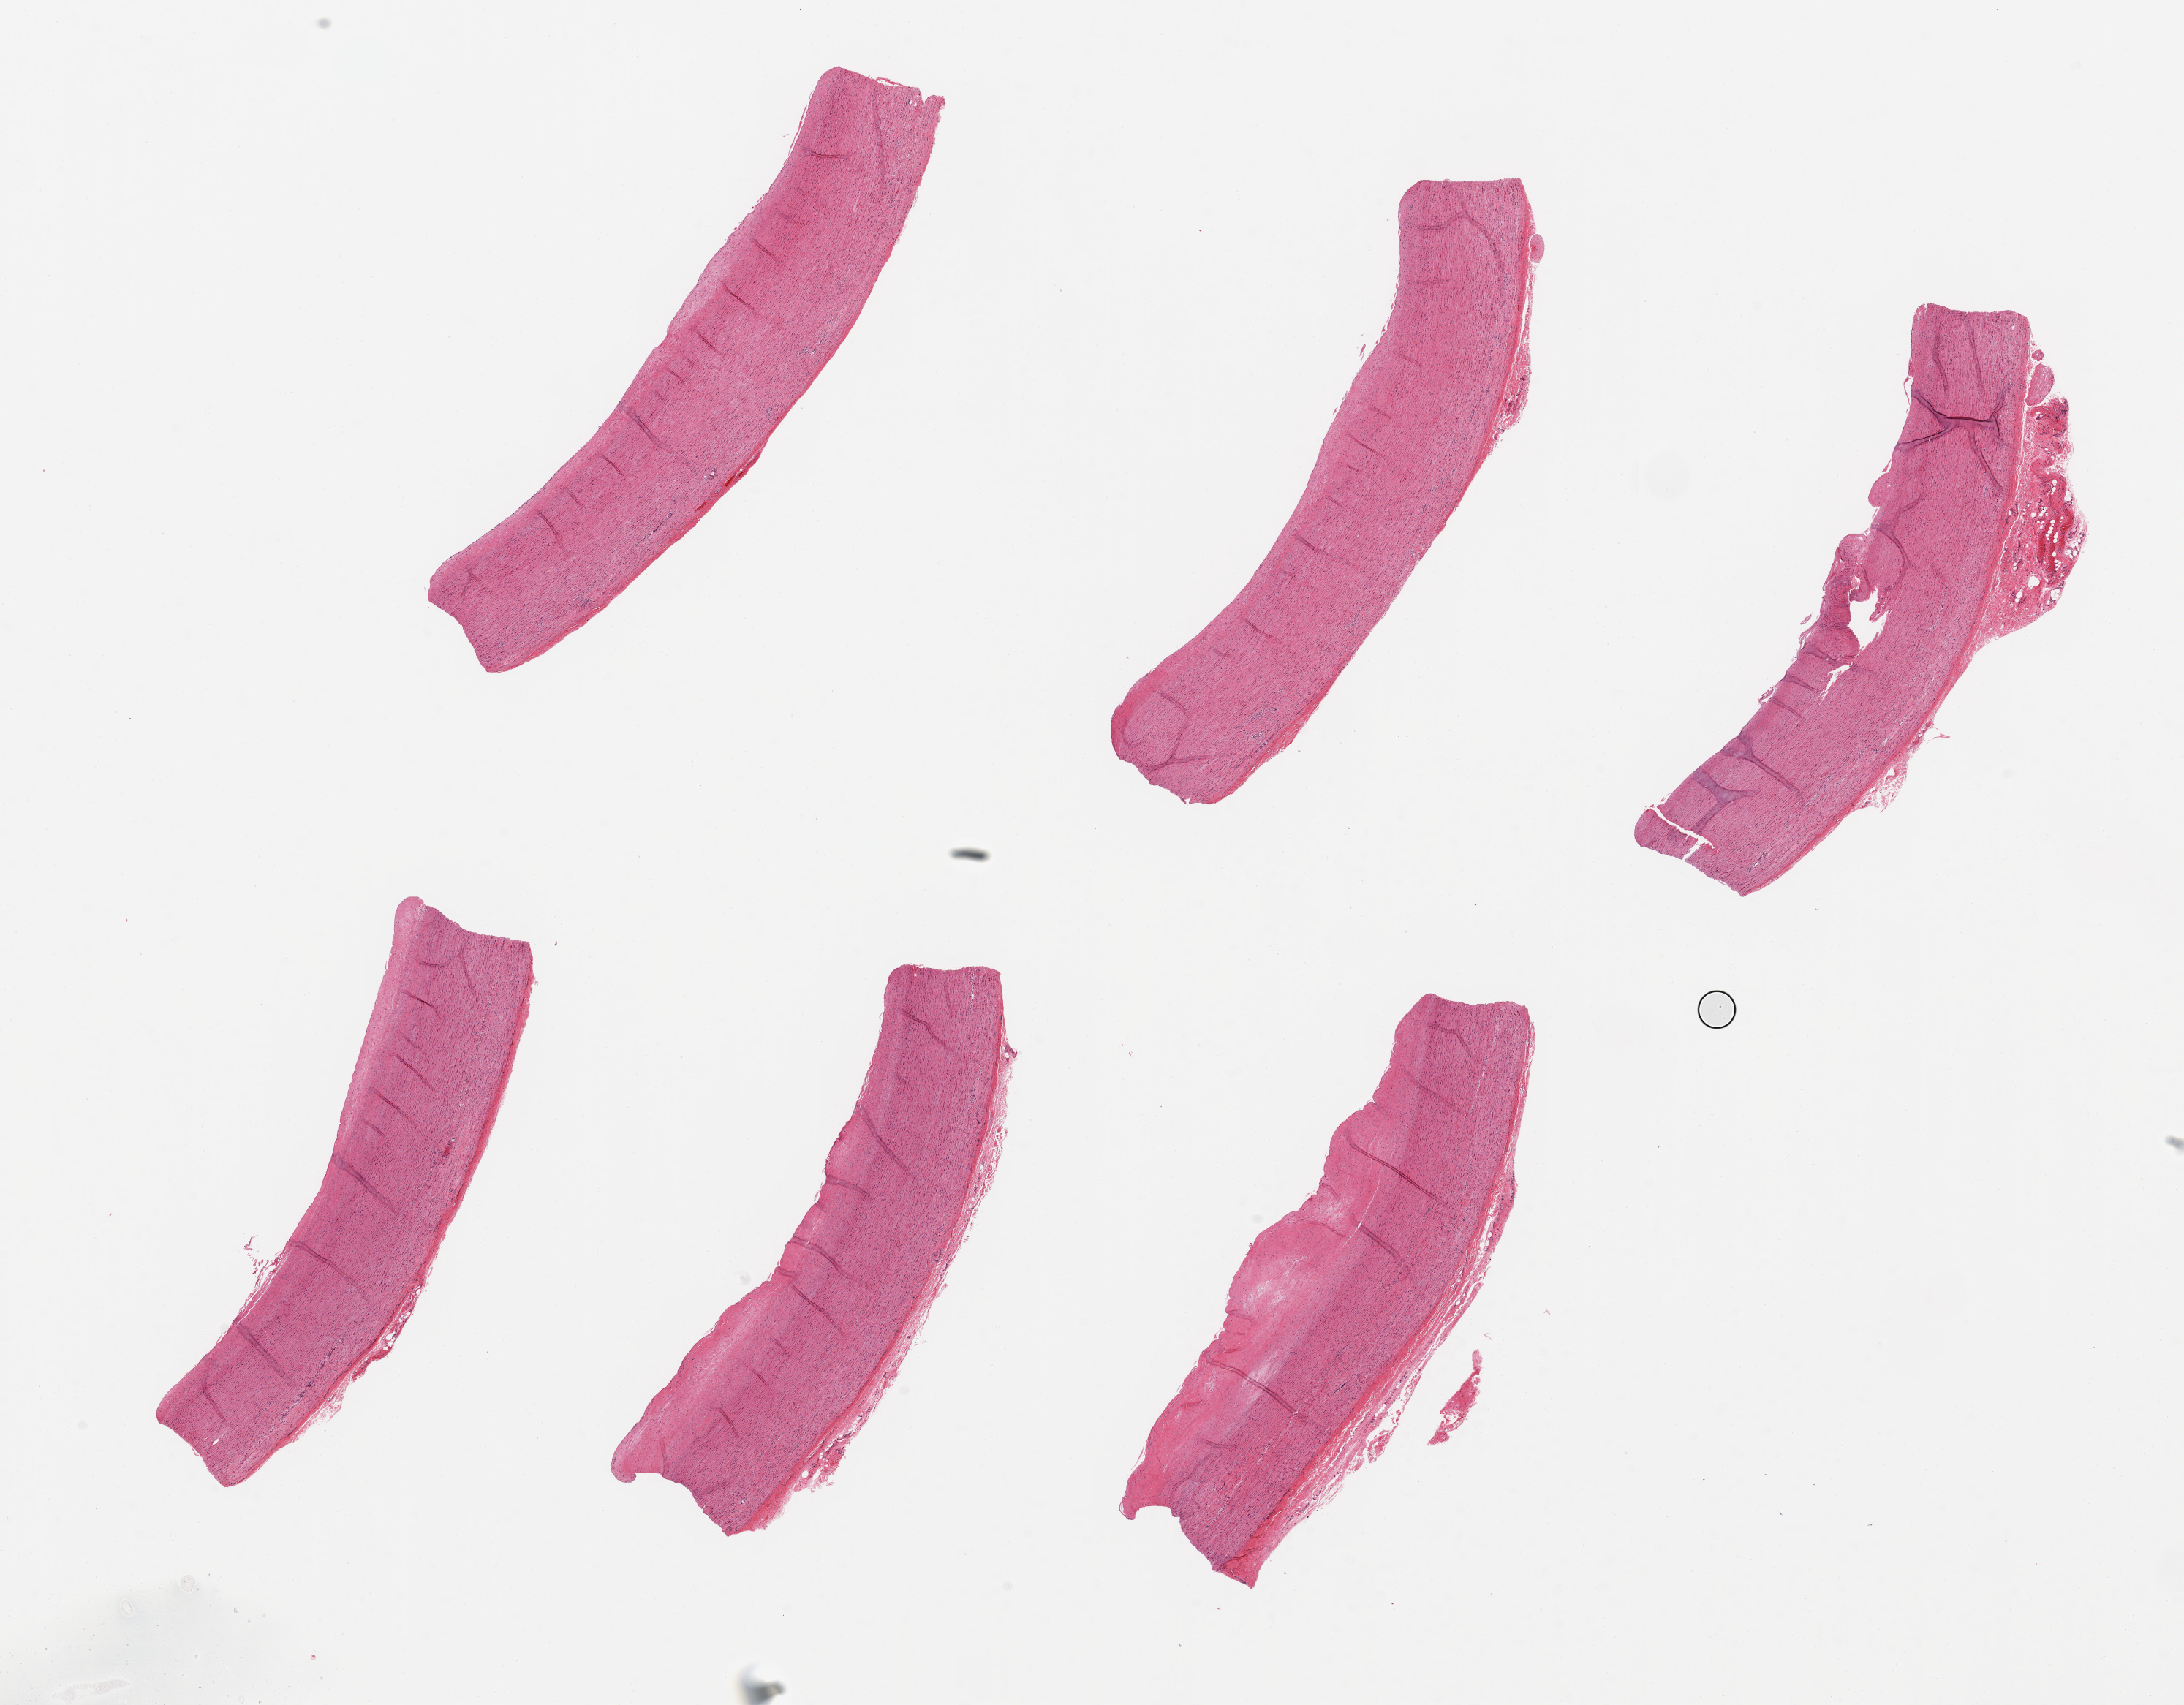
Haematoxylin and eosin whole-slide image, whole scanned area (about 23.6 x 18.4 mm, from a 20x scan) shown as a low-resolution overview, PAXgene-fixed, paraffin-embedded tissue, target tissue: aorta, tissue donor sample.
* reviewer comment on this tissue sample: 6 pieces ~7x1.5mm